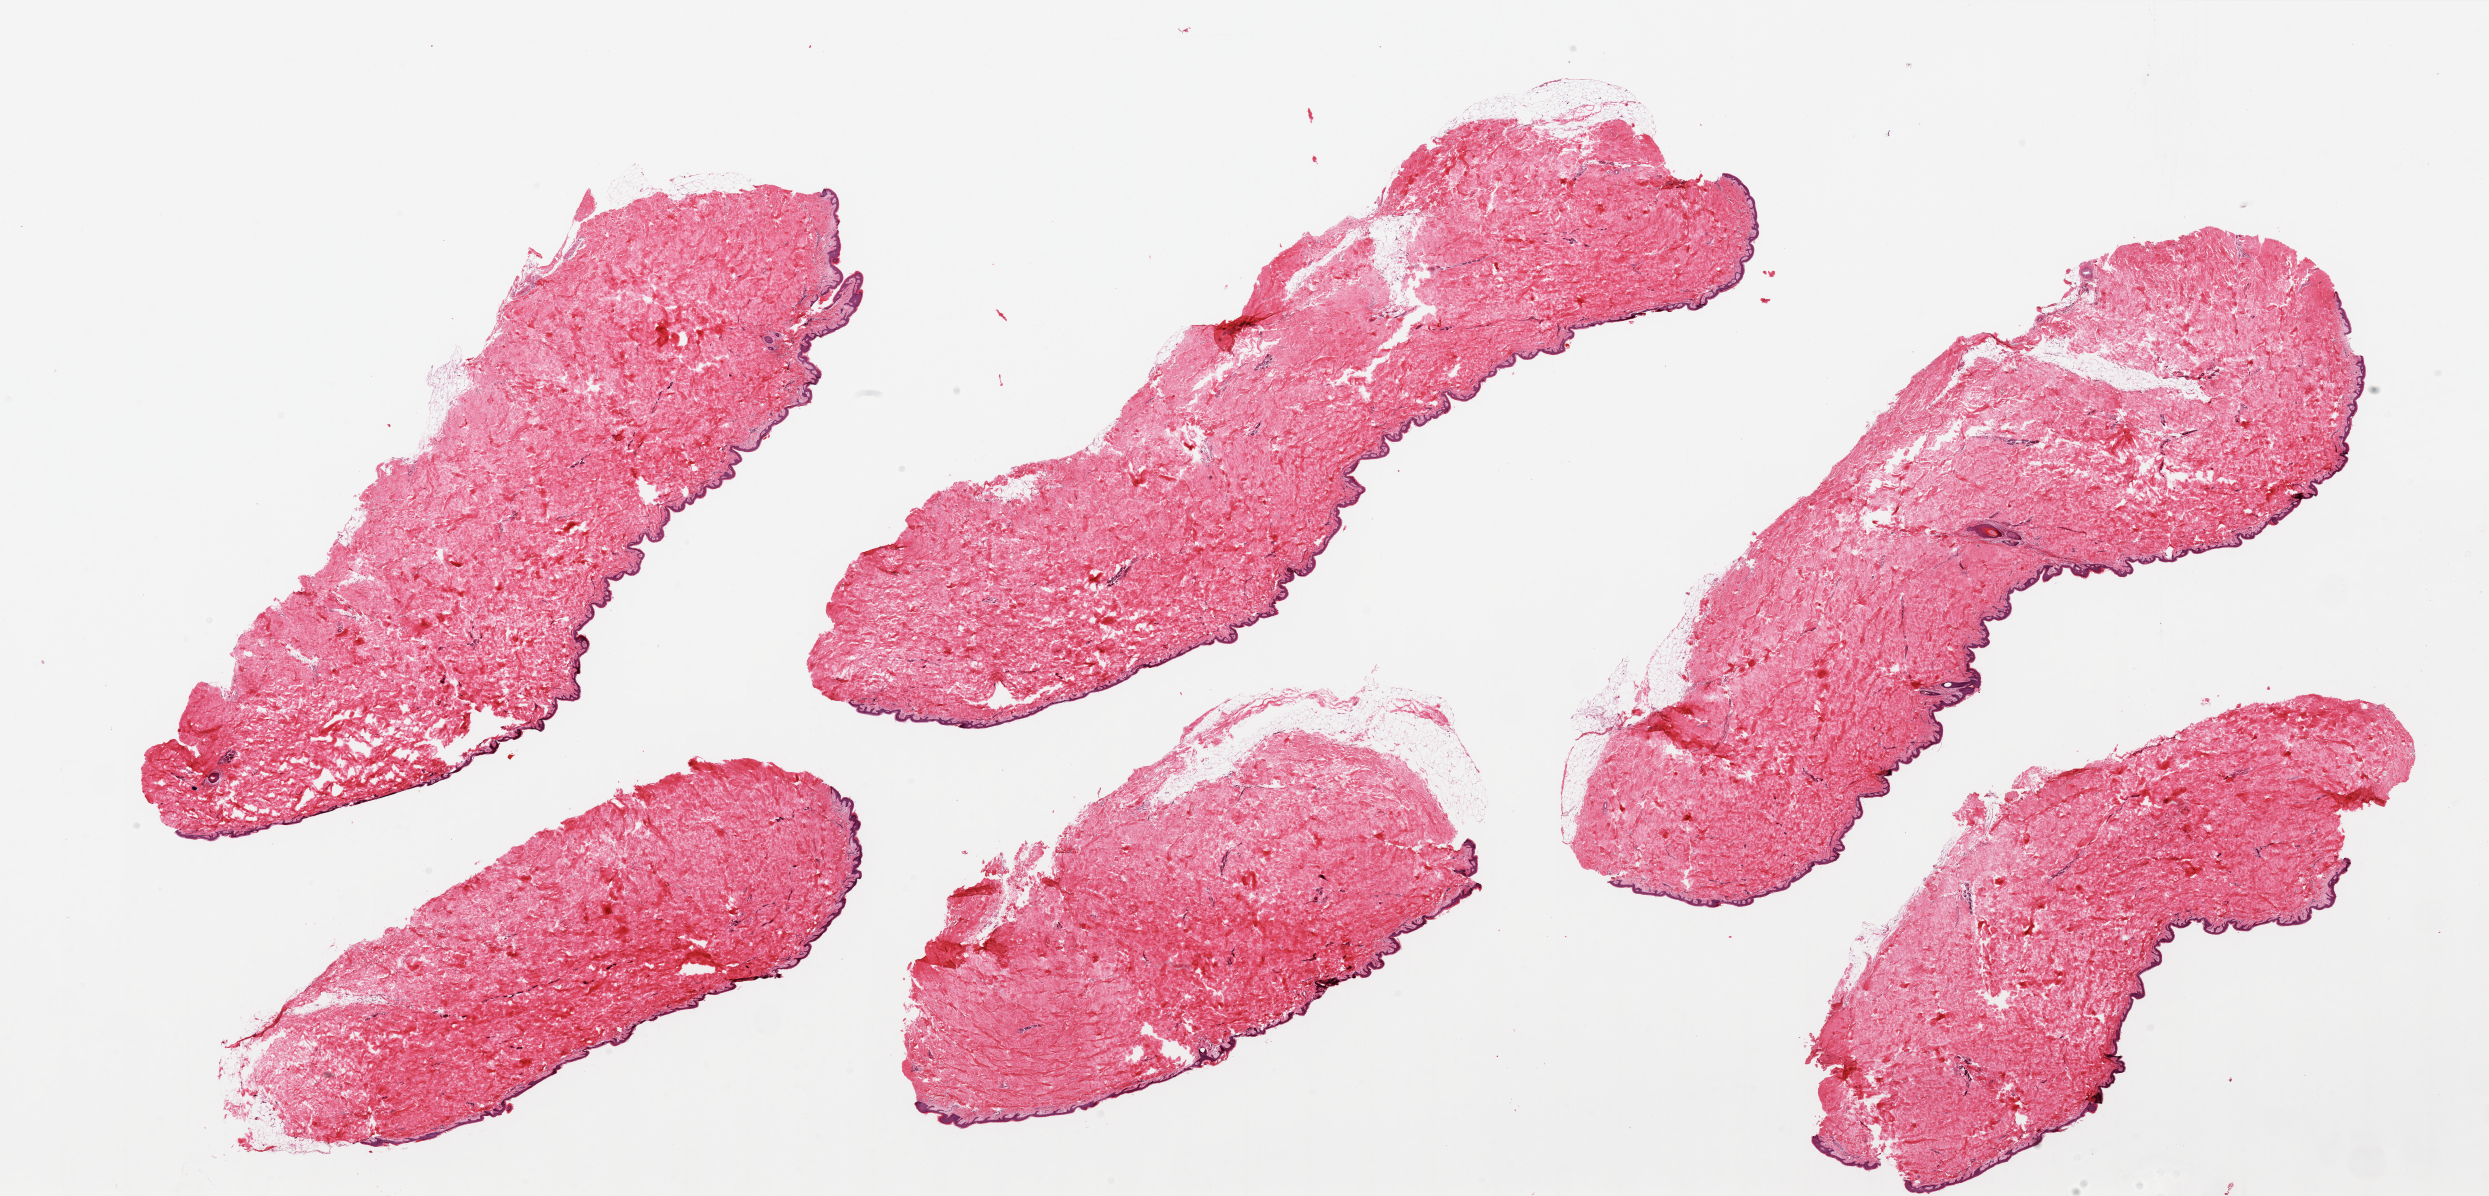
Hematoxylin and eosin (H&E) whole-slide image, low-resolution overview of the scanned area, about 39.4 x 18.9 mm. PAXgene-fixed, paraffin-embedded tissue. Sampled site (target tissue): skin of suprapubic region. Tissue donor sample. Donor sex: male.
Reviewer comment on this tissue sample: 6 pieces, well trimmed.